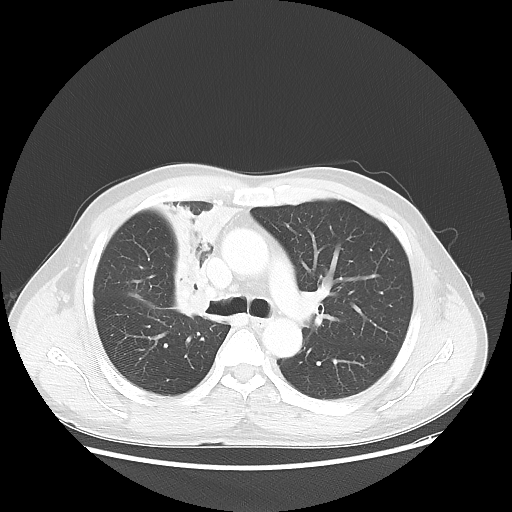
Chest CT, one axial slice; position 35 of 56 along the scan axis; 100 kVp; lung window (W 1500 / L -600 HU); 5 mm slice thickness; 512 × 512 image matrix. Patient: male, 60 years. From the clinical record (not read from this slice): clinical TNM (as recorded): T2a N1 M0.
Outlined on this slice (rectangle marked by the reading radiologist):
- lung tumour (recorded histology: squamous cell carcinoma): bounding box [x1, y1, x2, y2] px = [166, 192, 249, 336]